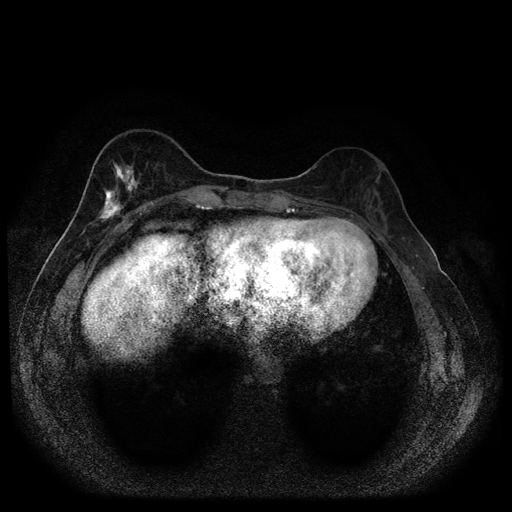
Breast MRI (dynamic contrast-enhanced, multi-phase), one axial slice; position 35 of 116 along the scan axis; dynamic contrast-enhanced series, time point 2 of 5 at this slice position (early post-contrast); 1.5 T; TE 2.7 ms, TR 5.4 ms; 2 mm slice thickness; 512 × 512 image matrix, field of view 330 × 330 mm. Patient: female, 49 years.
Outlined on this slice (semi-automatically segmented with operator editing):
- breast lesion (labelled 'tumour' in the annotation; benign lesions carry a separate 'benign' label): bounding box <95,159,142,226> (left, top, right, bottom; pixels)